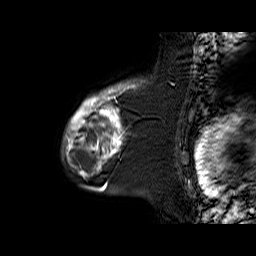
Breast MRI (dynamic contrast-enhanced), one sagittal slice. Position 50 of 60 along the scan axis. Dynamic contrast-enhanced series, time point 2 of 6 at this slice position (early post-contrast). 1.5 T. TE 6.3 ms, TR 32.9 ms. 4 mm slice thickness. 256 × 256 image matrix, field of view 200 × 200 mm. Female patient. From the clinical record (not read from this slice): setting: breast cancer imaged before/during neoadjuvant chemotherapy; receptor status: triple-negative.
Structures marked on this image (semi-automatically segmented with operator editing):
- analysis volume of interest (the breast-tissue region the enhancement analysis was run in; not a lesion): box from (x=62, y=83) to (x=145, y=170) px
- tumour enhancement mask (voxels above the 100 % enhancement threshold inside the analysis volume of interest): (x=64, y=83)–(x=131, y=170)